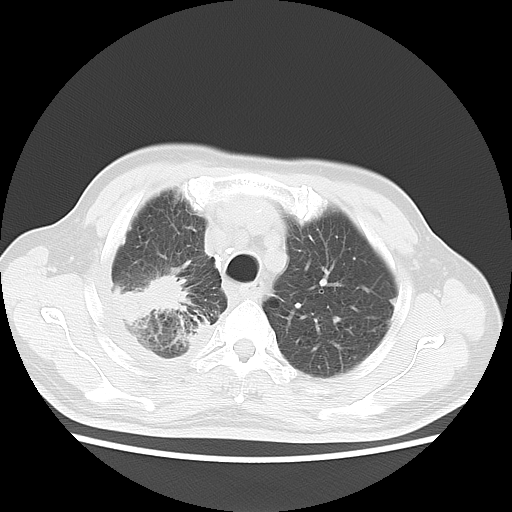
Chest CT, one axial slice; slice 13 of 16 in the series (ordered by position); reconstruction kernel LUNG; 120 kVp; lung window (W 1500 / L -600 HU); 5 mm slice thickness; 512 × 512 image matrix, field of view 350 × 350 mm. Patient: male, 75 years. Case-level facts recorded for this patient, not image findings: clinical TNM (as recorded): T1c N1 M1.
Outlined on this slice (rectangle marked by the reading radiologist):
- lung tumour (recorded histology: adenocarcinoma): bounding box (x1, y1, x2, y2) in pixels: (105, 272, 203, 333)